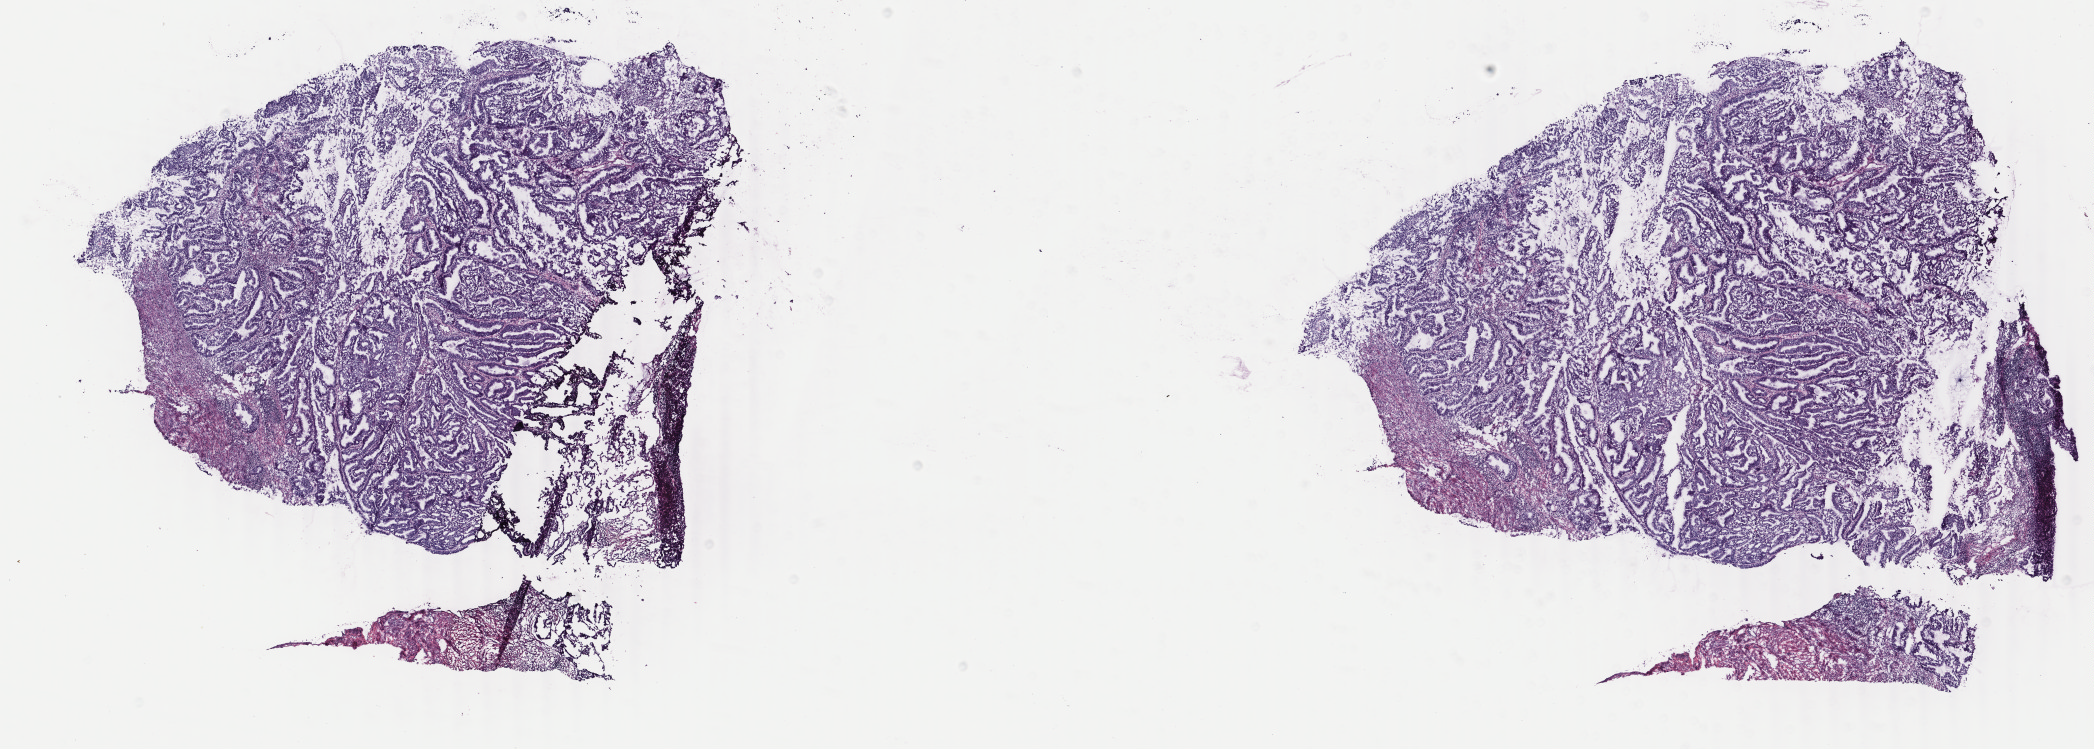
Whole-slide histology image, H&E, low-resolution overview of the scanned area, about 16.7 x 6.0 mm (slide scanned at 40x); frozen section; uterus, primary tumour sample. Patient: female, age at initial diagnosis 53 years. Histologic grade: G2 (moderately differentiated). Pathologist review of this section (percent, as recorded): tumour cells 90%, tumour nuclei 85%, normal cells 10%, stromal cells 0%, necrosis 0%. Infiltration values recorded for this section: lymphocyte infiltration 0%, monocyte infiltration 0%, neutrophil infiltration 0%.
* FIGO stage: IA
* diagnosis: Endometrioid adenocarcinoma, NOS (endometrium)